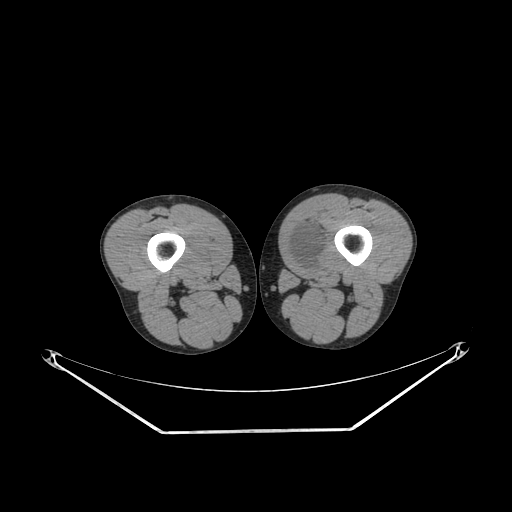
CT of an extremity soft-tissue mass (from a PET/CT study), one axial slice; slice 233 of 311 in the series (ordered by position); reconstruction kernel SOFT; 140 kVp; soft-tissue window (W 400 / L 40 HU); 512 × 512 image matrix. Male patient. Case-level facts recorded for this patient, not image findings: histological type: mixoid liposarcoma; grade: low; site of the primary tumour: left thigh.
Outlined on this slice (expert contour drawn on MRI and transferred to this co-registered scan by the dataset authors):
- gross tumour volume (mass): bounding box [x1, y1, x2, y2] px = [285, 226, 327, 275]